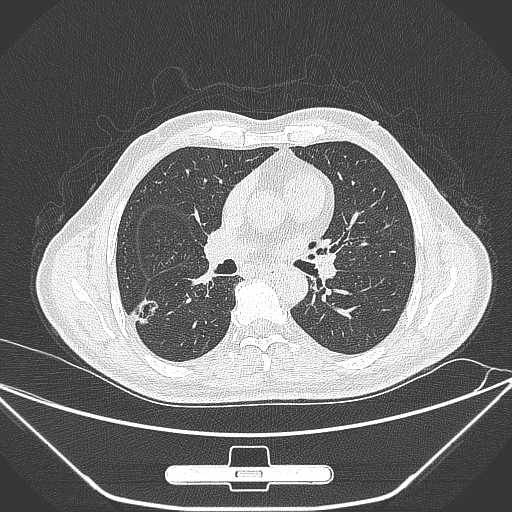
Chest CT, one axial slice; position 153 of 309 along the scan axis; 120 kVp; lung window (W 1500 / L -600 HU); 1 mm slice thickness; 512 × 512 image matrix, field of view 398 × 398 mm. Male patient, age 71 years. Case-level facts recorded for this patient, not image findings: clinical TNM (as recorded): T1c N0 M0; histopathological grade: G2.
Outlined on this slice (rectangle marked by the reading radiologist):
- lung tumour (recorded histology: adenocarcinoma): bounding box [x1, y1, x2, y2] px = [126, 293, 163, 334]